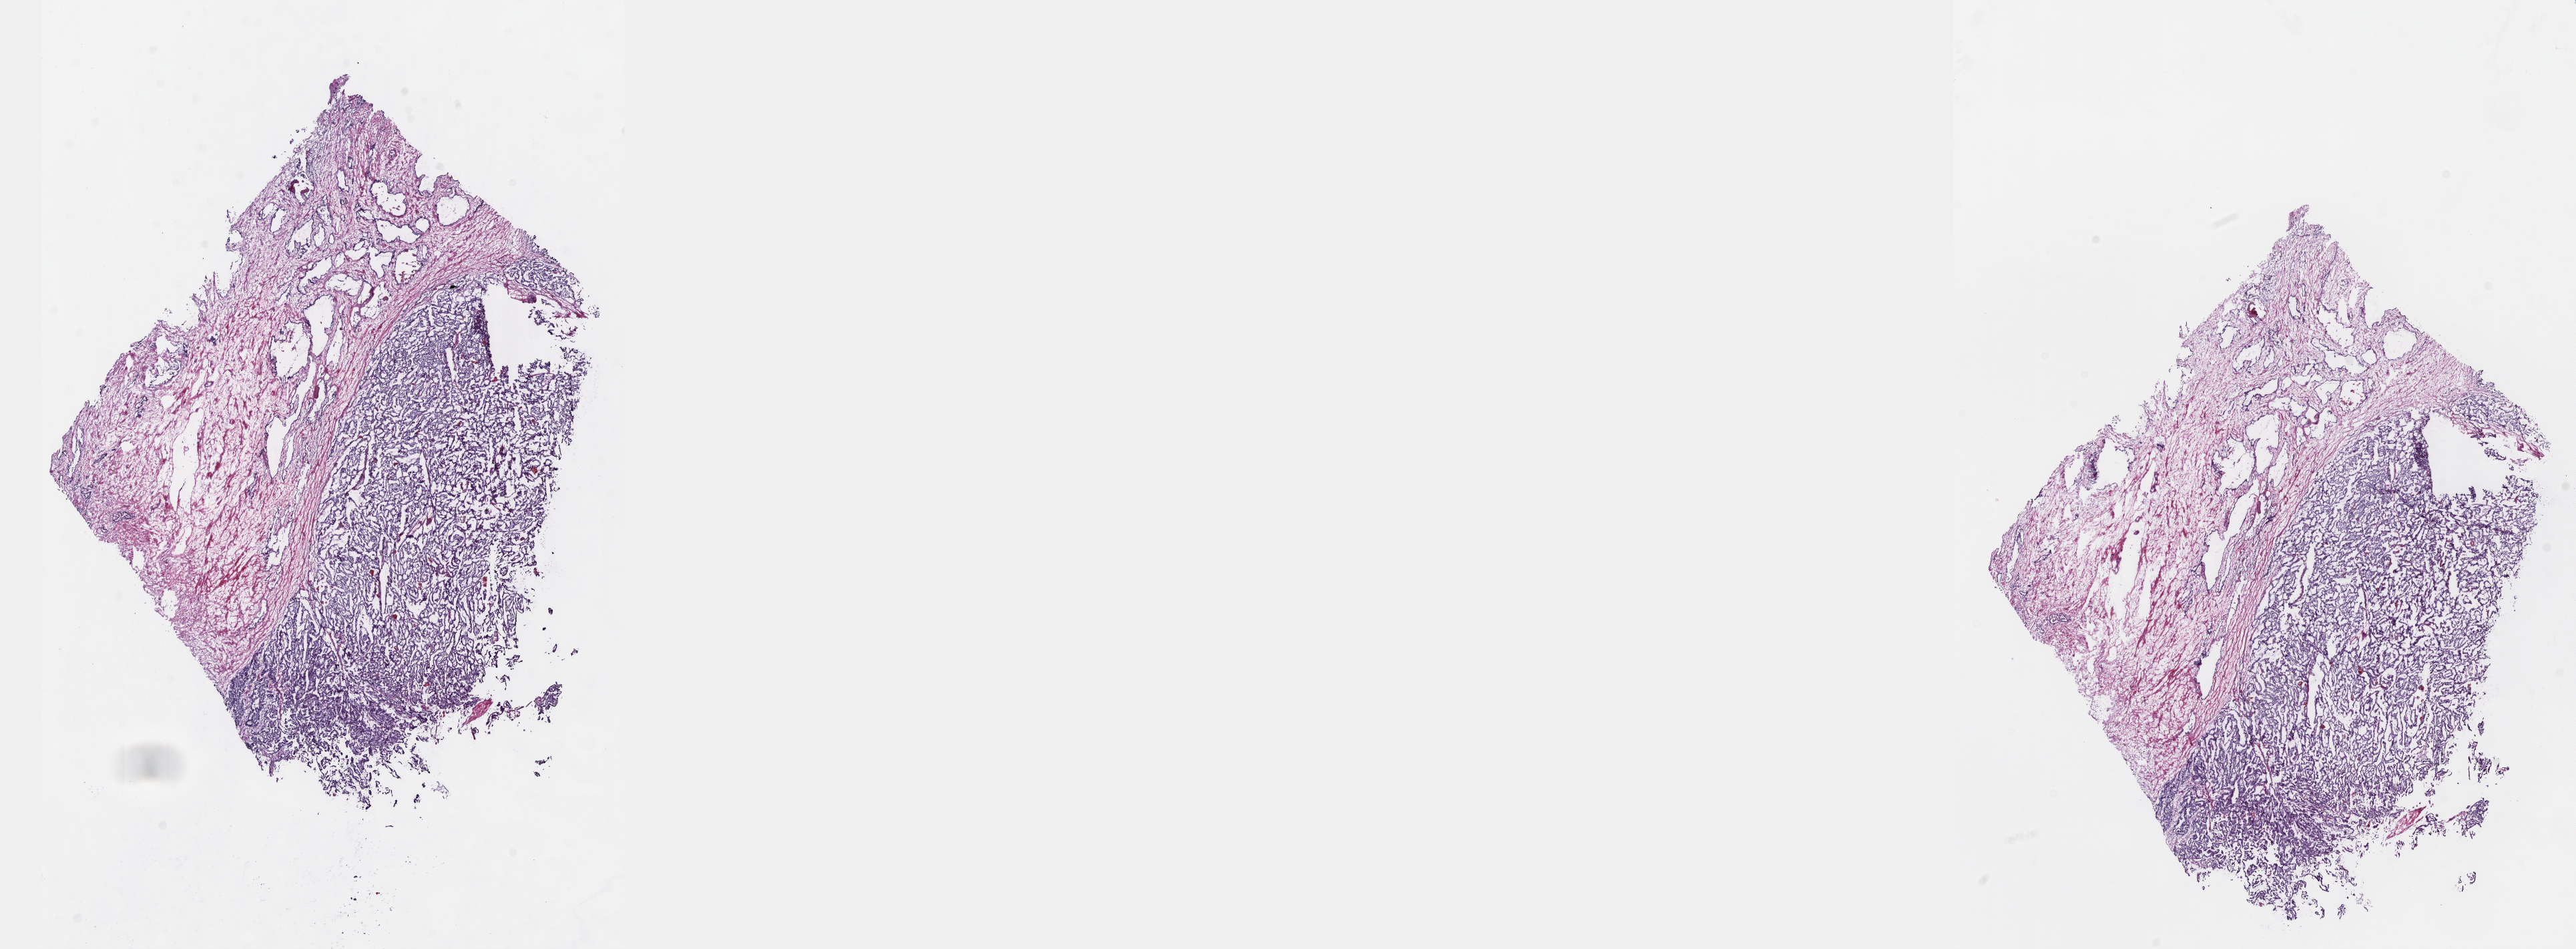
Digitized H&E tissue section (whole slide), a low-resolution overview of the entire scanned area, about 31.2 x 11.5 mm (from a 40x scan). Frozen section from the top of the tissue portion. Sample: primary tumour, prostate. Male, age 66 years at initial diagnosis. Gleason score: 7 (3+4). Composition of this section per pathologist review: tumour cells 50%, tumour nuclei 60%, normal cells 50%, stromal cells 0%, necrosis 0%. Infiltration values recorded for this section: lymphocyte infiltration 0%, monocyte infiltration 0%, neutrophil infiltration 0%.
Lymph nodes positive (case pathology): 0 of 69 examined. Laterality: bilateral. Diagnosis: Adenocarcinoma, NOS (prostate gland).